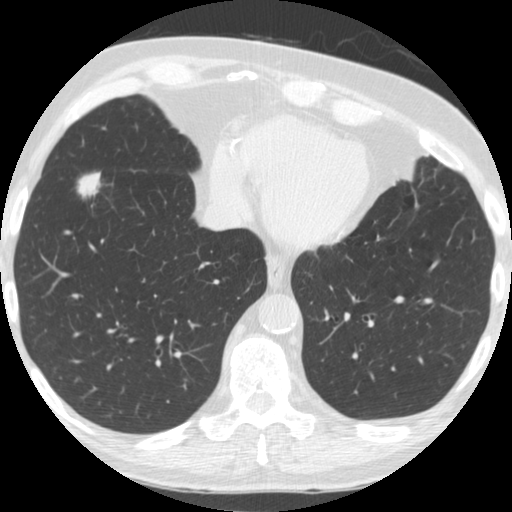
Low-dose screening chest CT, one axial slice. Position 65 of 182 along the scan axis. Reconstruction kernel STANDARD. 120 kVp. Lung window (W 1500 / L -600 HU). 512 × 512 image matrix.
Structures marked on this image (outlined manually by an expert reader):
- lesion 1 (tumor, lower lobe of right lung): bounding box [x1, y1, x2, y2] px = [77, 172, 101, 198]